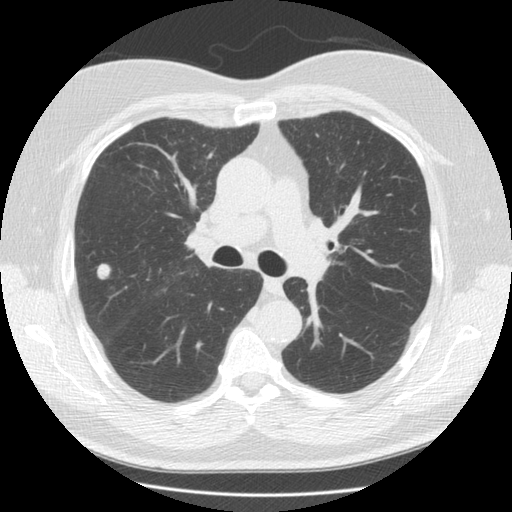
Chest CT (low-dose screening protocol), one axial image. Third screening round (two years after baseline). Lung window (W 1500 / L -600 HU). 2.5 mm slice thickness. Slice 58 of 146 in the series. Male participant, aged 65 years at enrolment. Former smoker at enrolment.
• Lesion marked by an expert reader, bounding box (x1, y1, x2, y2) in pixels: (90, 258, 117, 287).
• Screening reader's record for this exam (one nodule recorded; not confirmed to be the boxed lesion): non-calcified nodule or mass ≥4 mm, right upper lobe, 12 × 12 mm, smooth margins, soft tissue attenuation, pre-existing on the prior screen: yes; interval growth: yes.
• Lung cancer was diagnosed 54 days after this screen: adenocarcinoma, NOS, right upper lobe, poorly differentiated (G3), stage IA (AJCC 6th edition), 17 mm at pathology.